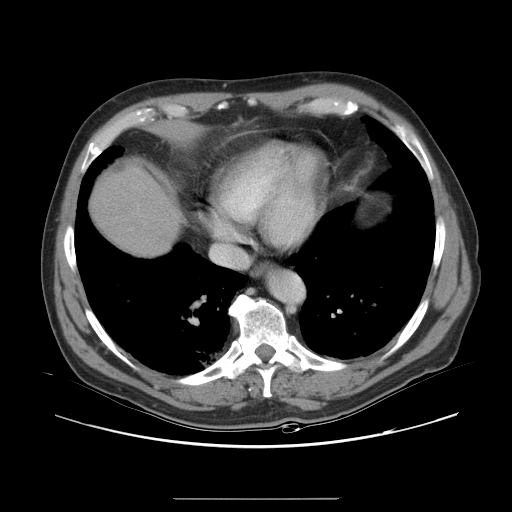
Contrast-enhanced abdominal CT, one axial slice. Slice 31 of 40 in the series (ordered by position). 120 kVp. Intravenous contrast given. Soft-tissue window (W 400 / L 40 HU). 5 mm slice thickness. 512 × 512 image matrix, field of view 408 × 408 mm. Male patient, age 64 years. From the clinical record (not read from this slice): diagnosis: colorectal cancer liver metastases, imaged before liver resection; multiple liver metastases: yes; largest metastasis: 3.2 cm.
Annotated regions visible in this slice (outlined manually by an expert reader):
- liver: bounding box [x1, y1, x2, y2] px = [94, 168, 178, 255]
- planned liver remnant (the part of the liver to remain after resection): [93, 168, 178, 256]